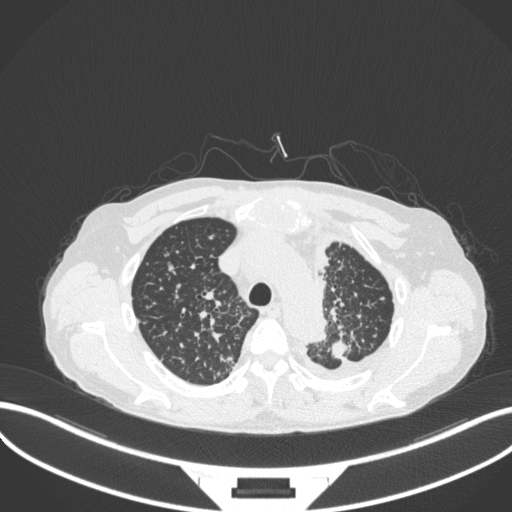
Chest CT, one axial slice; position 273 of 319 along the scan axis; reconstruction kernel B31f; lung window (W 1500 / L -600 HU); 1 mm slice thickness; 512 × 512 image matrix. Patient: male, 58 years. From the clinical record (not read from this slice): clinical TNM (as recorded): T1c N3 M1.
Structures marked on this image (rectangle marked by the reading radiologist):
- lung tumour (recorded histology: adenocarcinoma): bounding box [x1, y1, x2, y2] px = [326, 337, 353, 361]